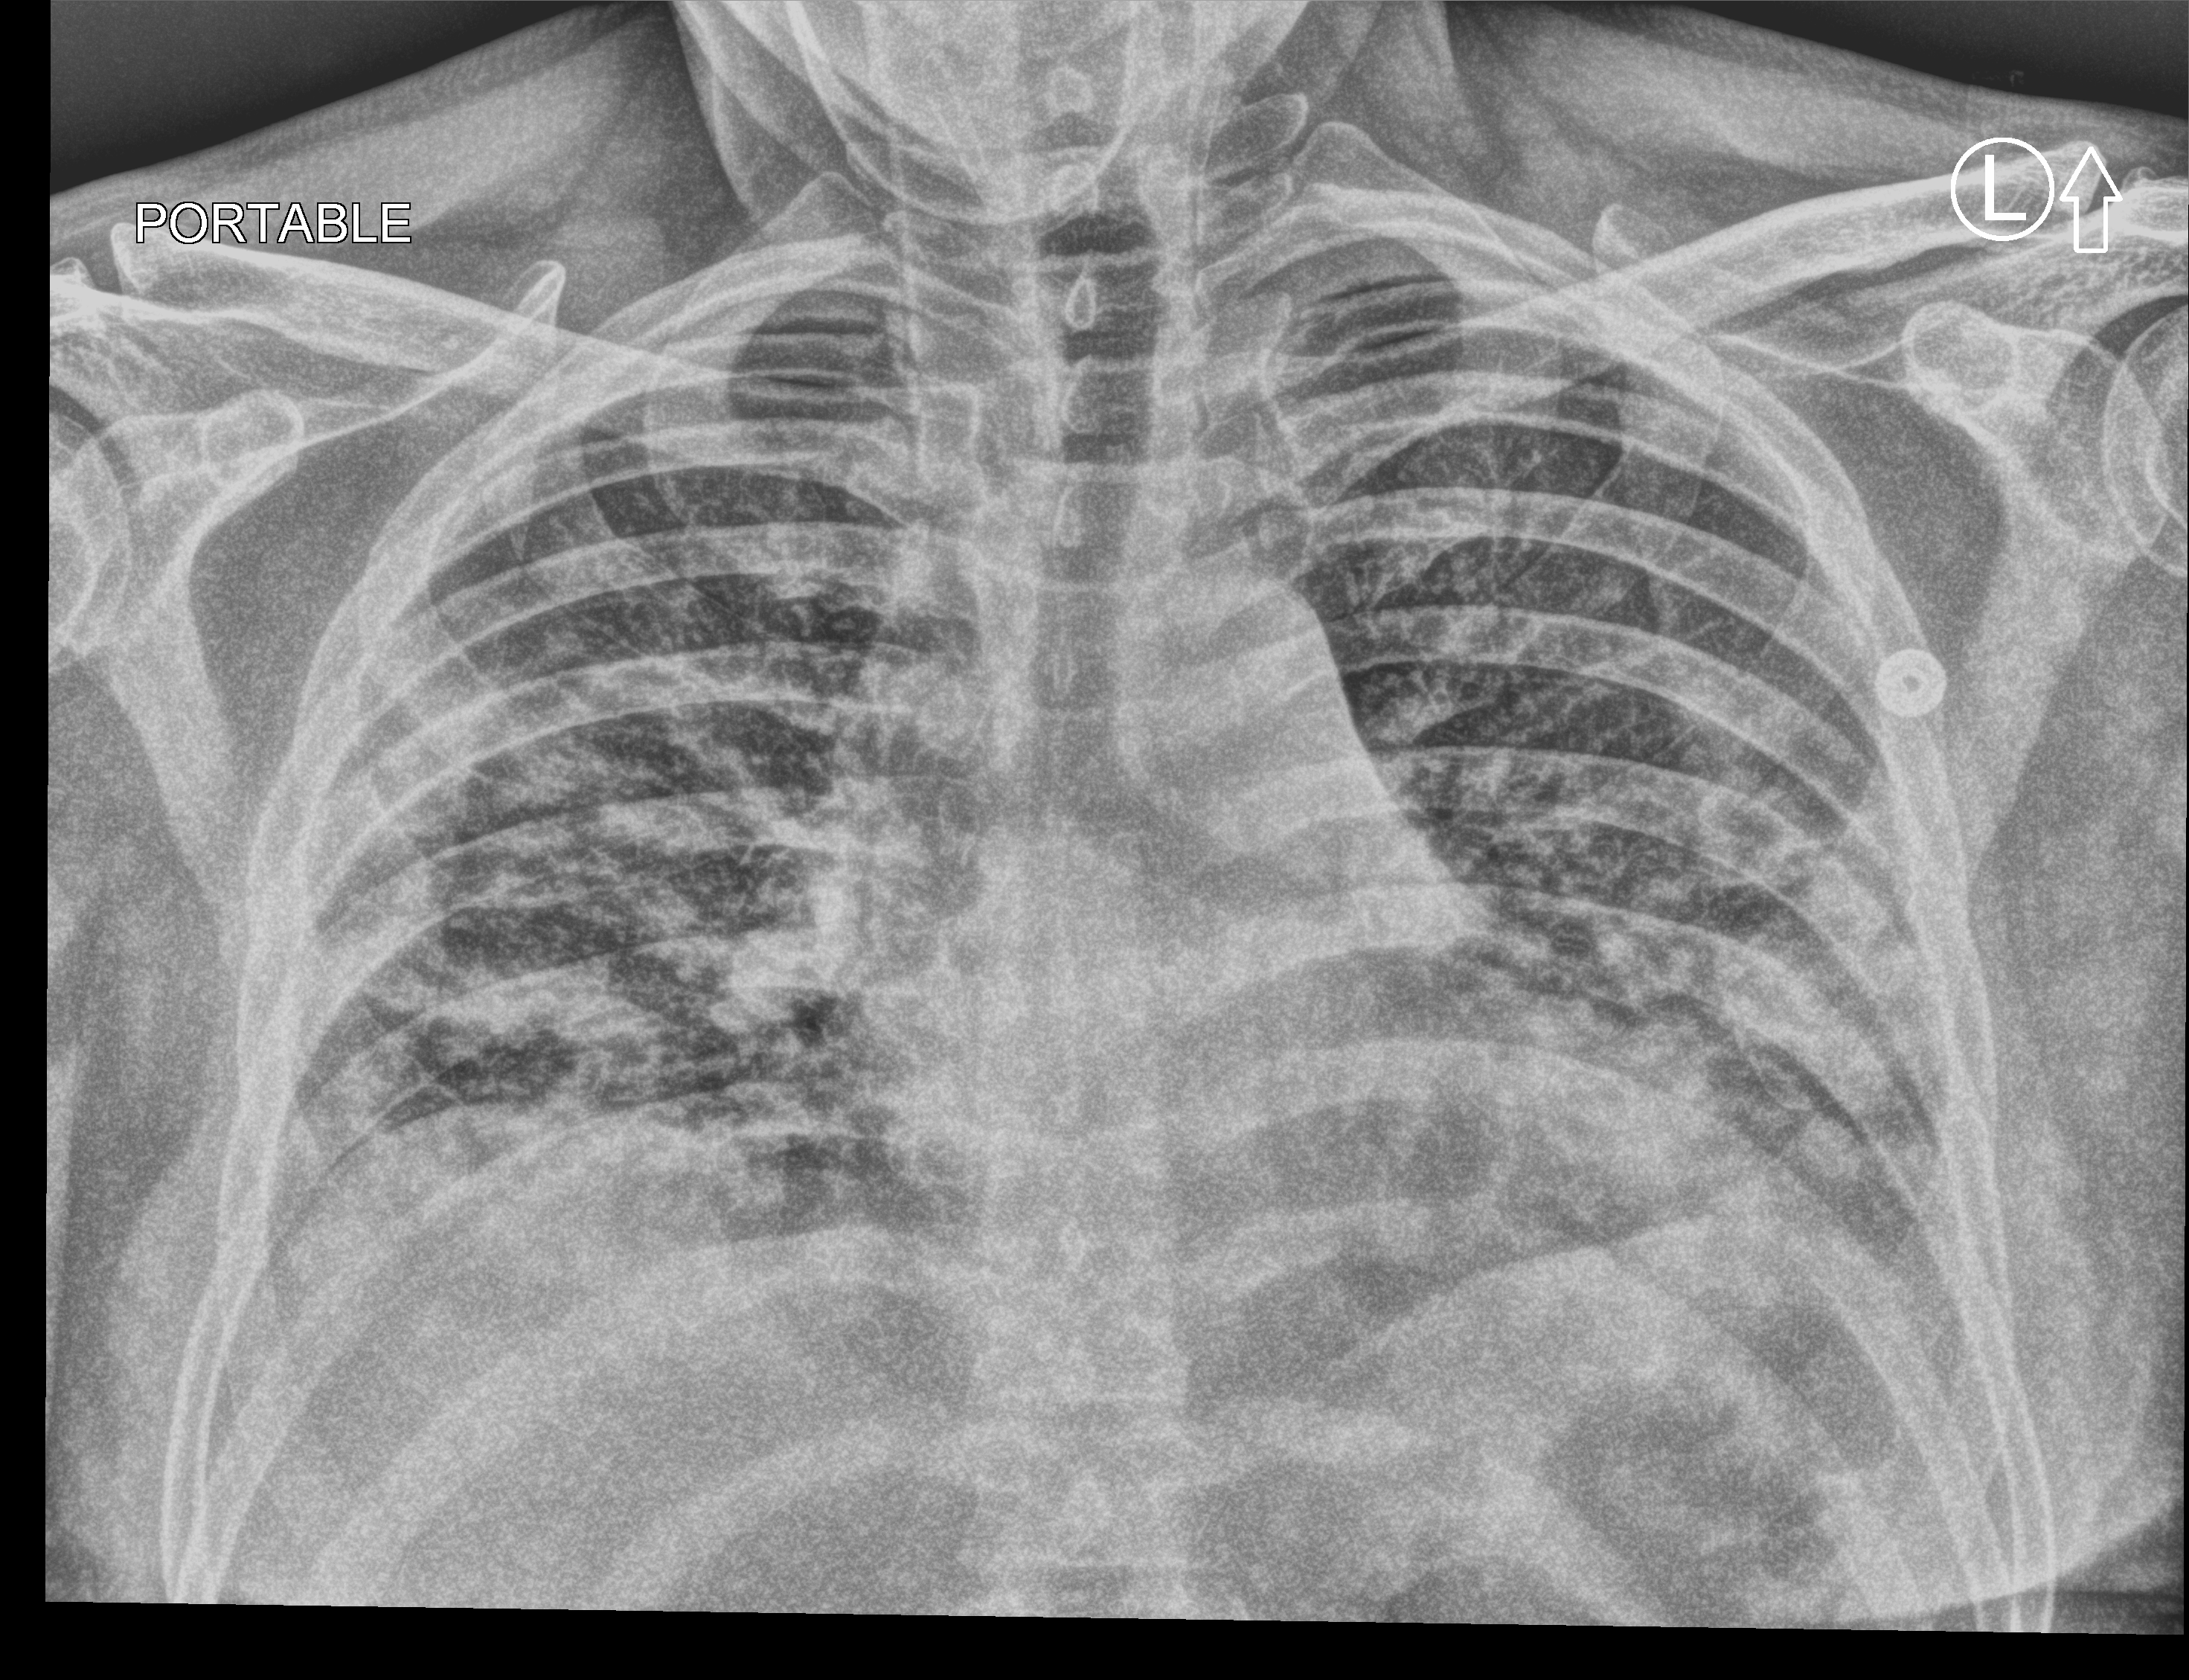
Chest X-ray (portable); anteroposterior (AP) projection. Patient hospitalised with COVID-19; male, aged 60–74 years.
From the hospital-stay record, not from the radiograph (when in the stay this image was taken is not recorded):
- mechanically ventilated during this hospital stay: no
- admitted to intensive care during this hospital stay: no
- smoking status (admission record): never